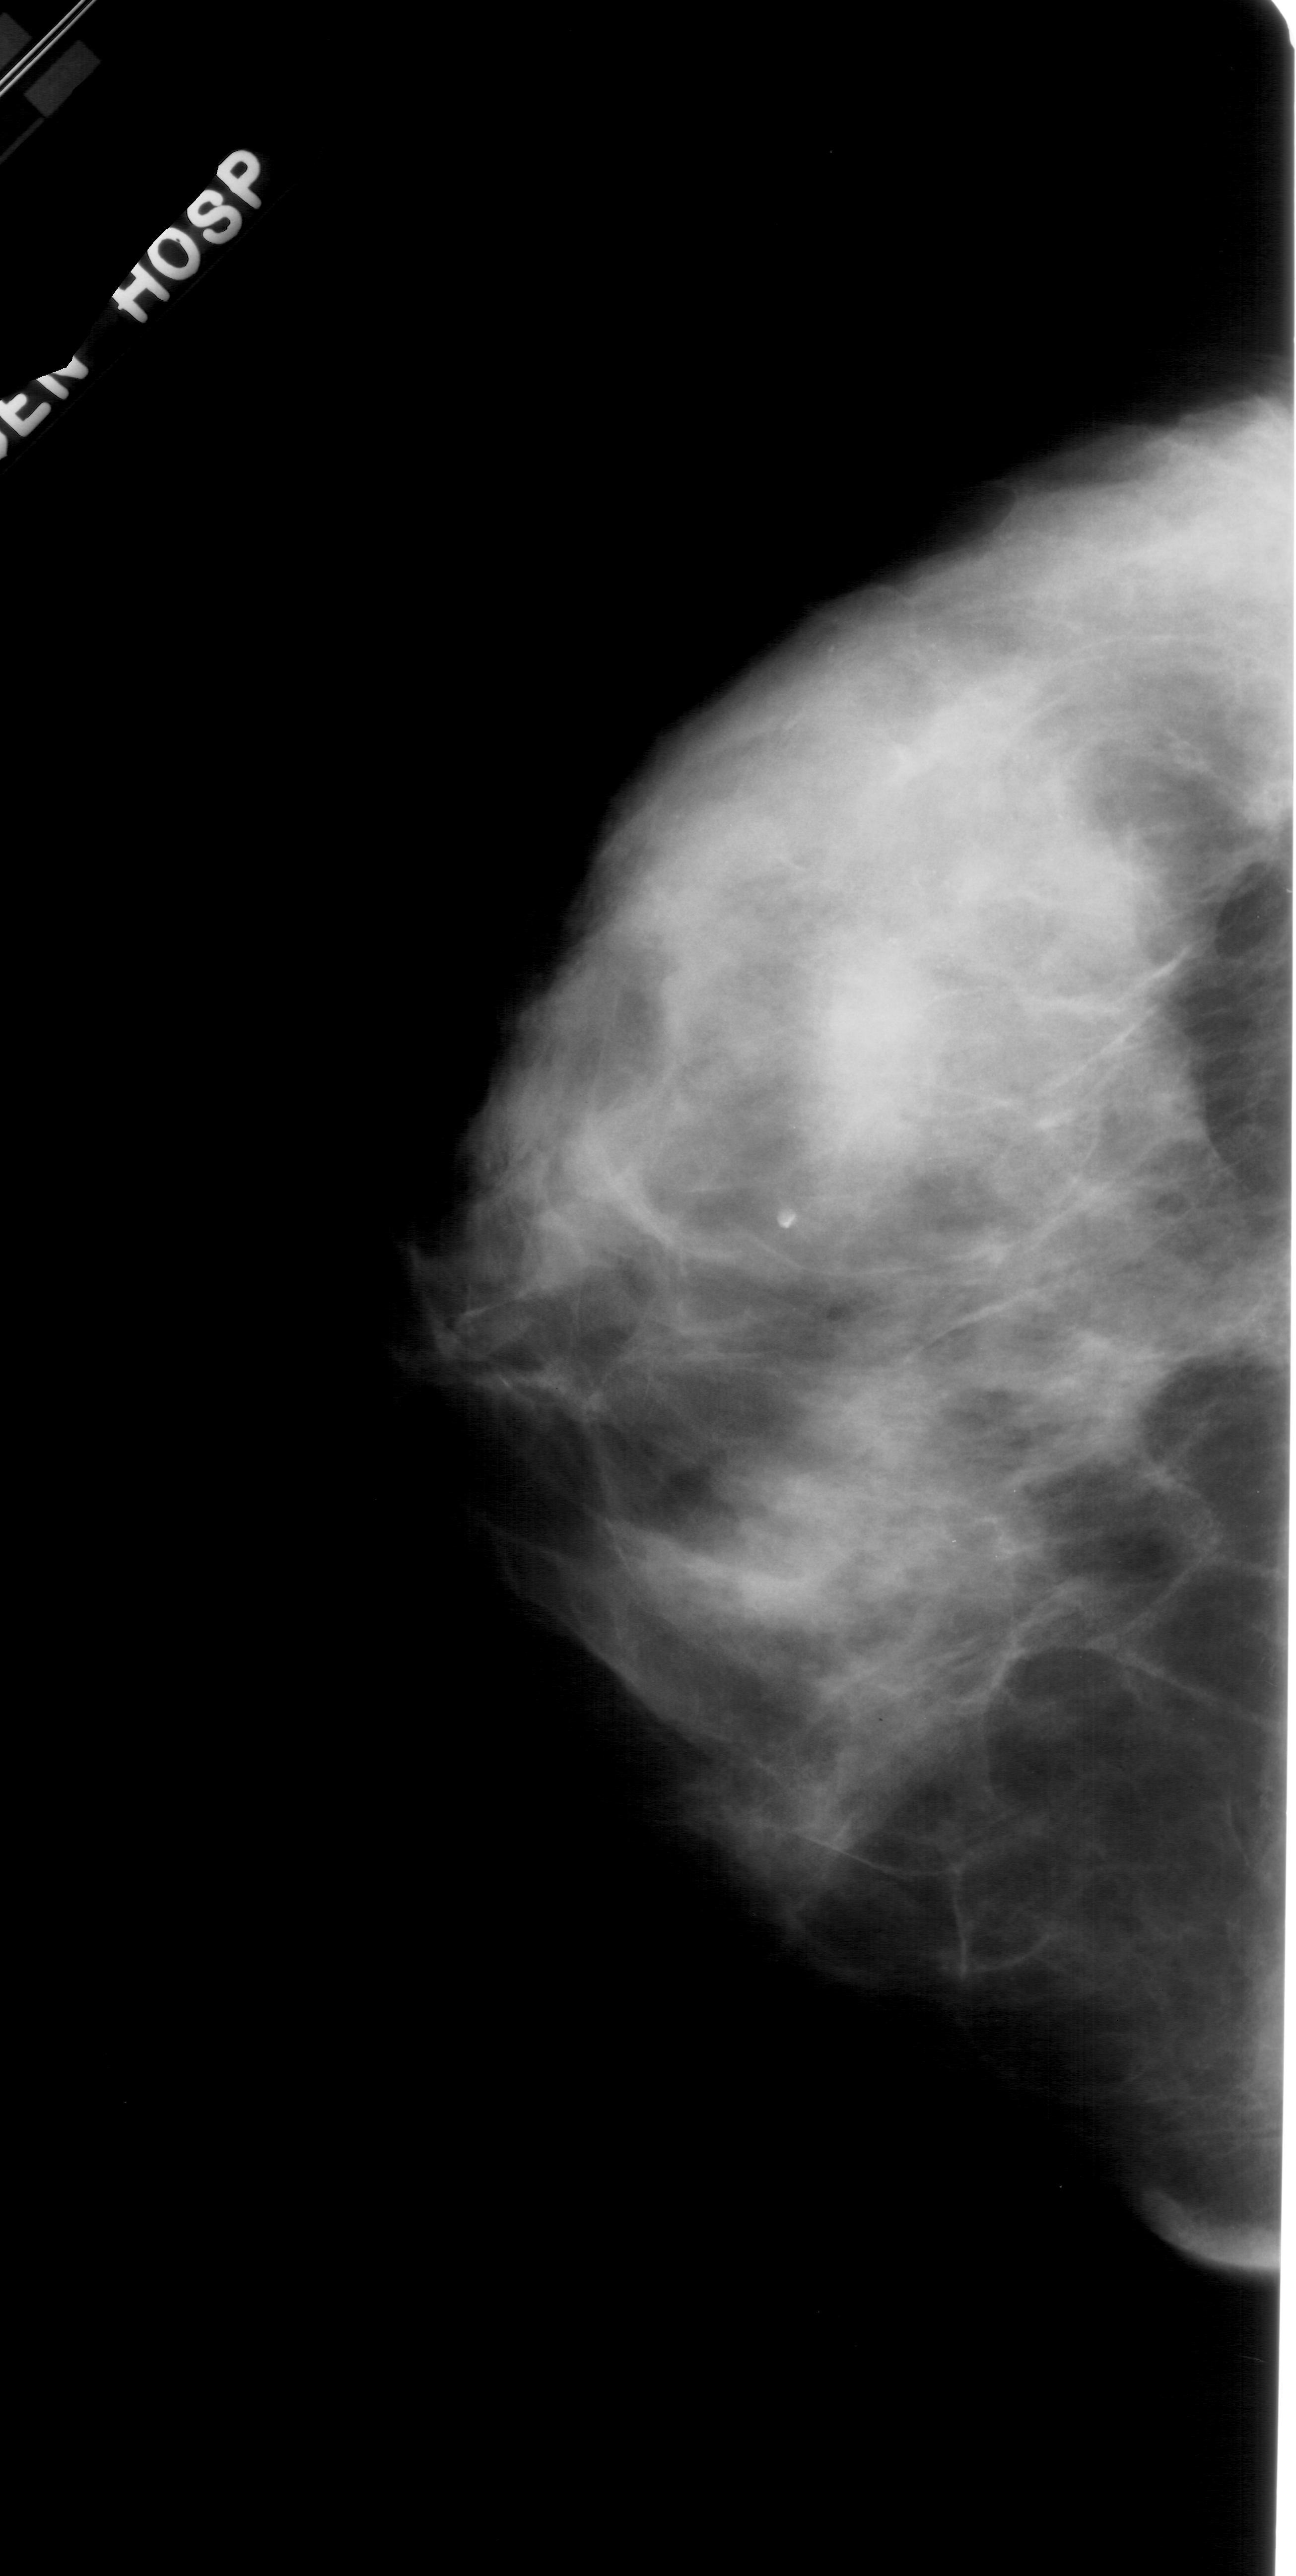
Scanned film-screen mammogram. Left breast. CC view. Breast composition: extremely dense (BI-RADS density category 4 of 4). 1296 × 2576 image matrix.
Marked abnormalities (boxes around the expert regions of interest):
- calcifications, morphology punctate, distribution segmental; BI-RADS assessment category 4; pathology result (as recorded, not read from the image): benign: bounding box <878,627,1141,1054> (left, top, right, bottom; pixels)